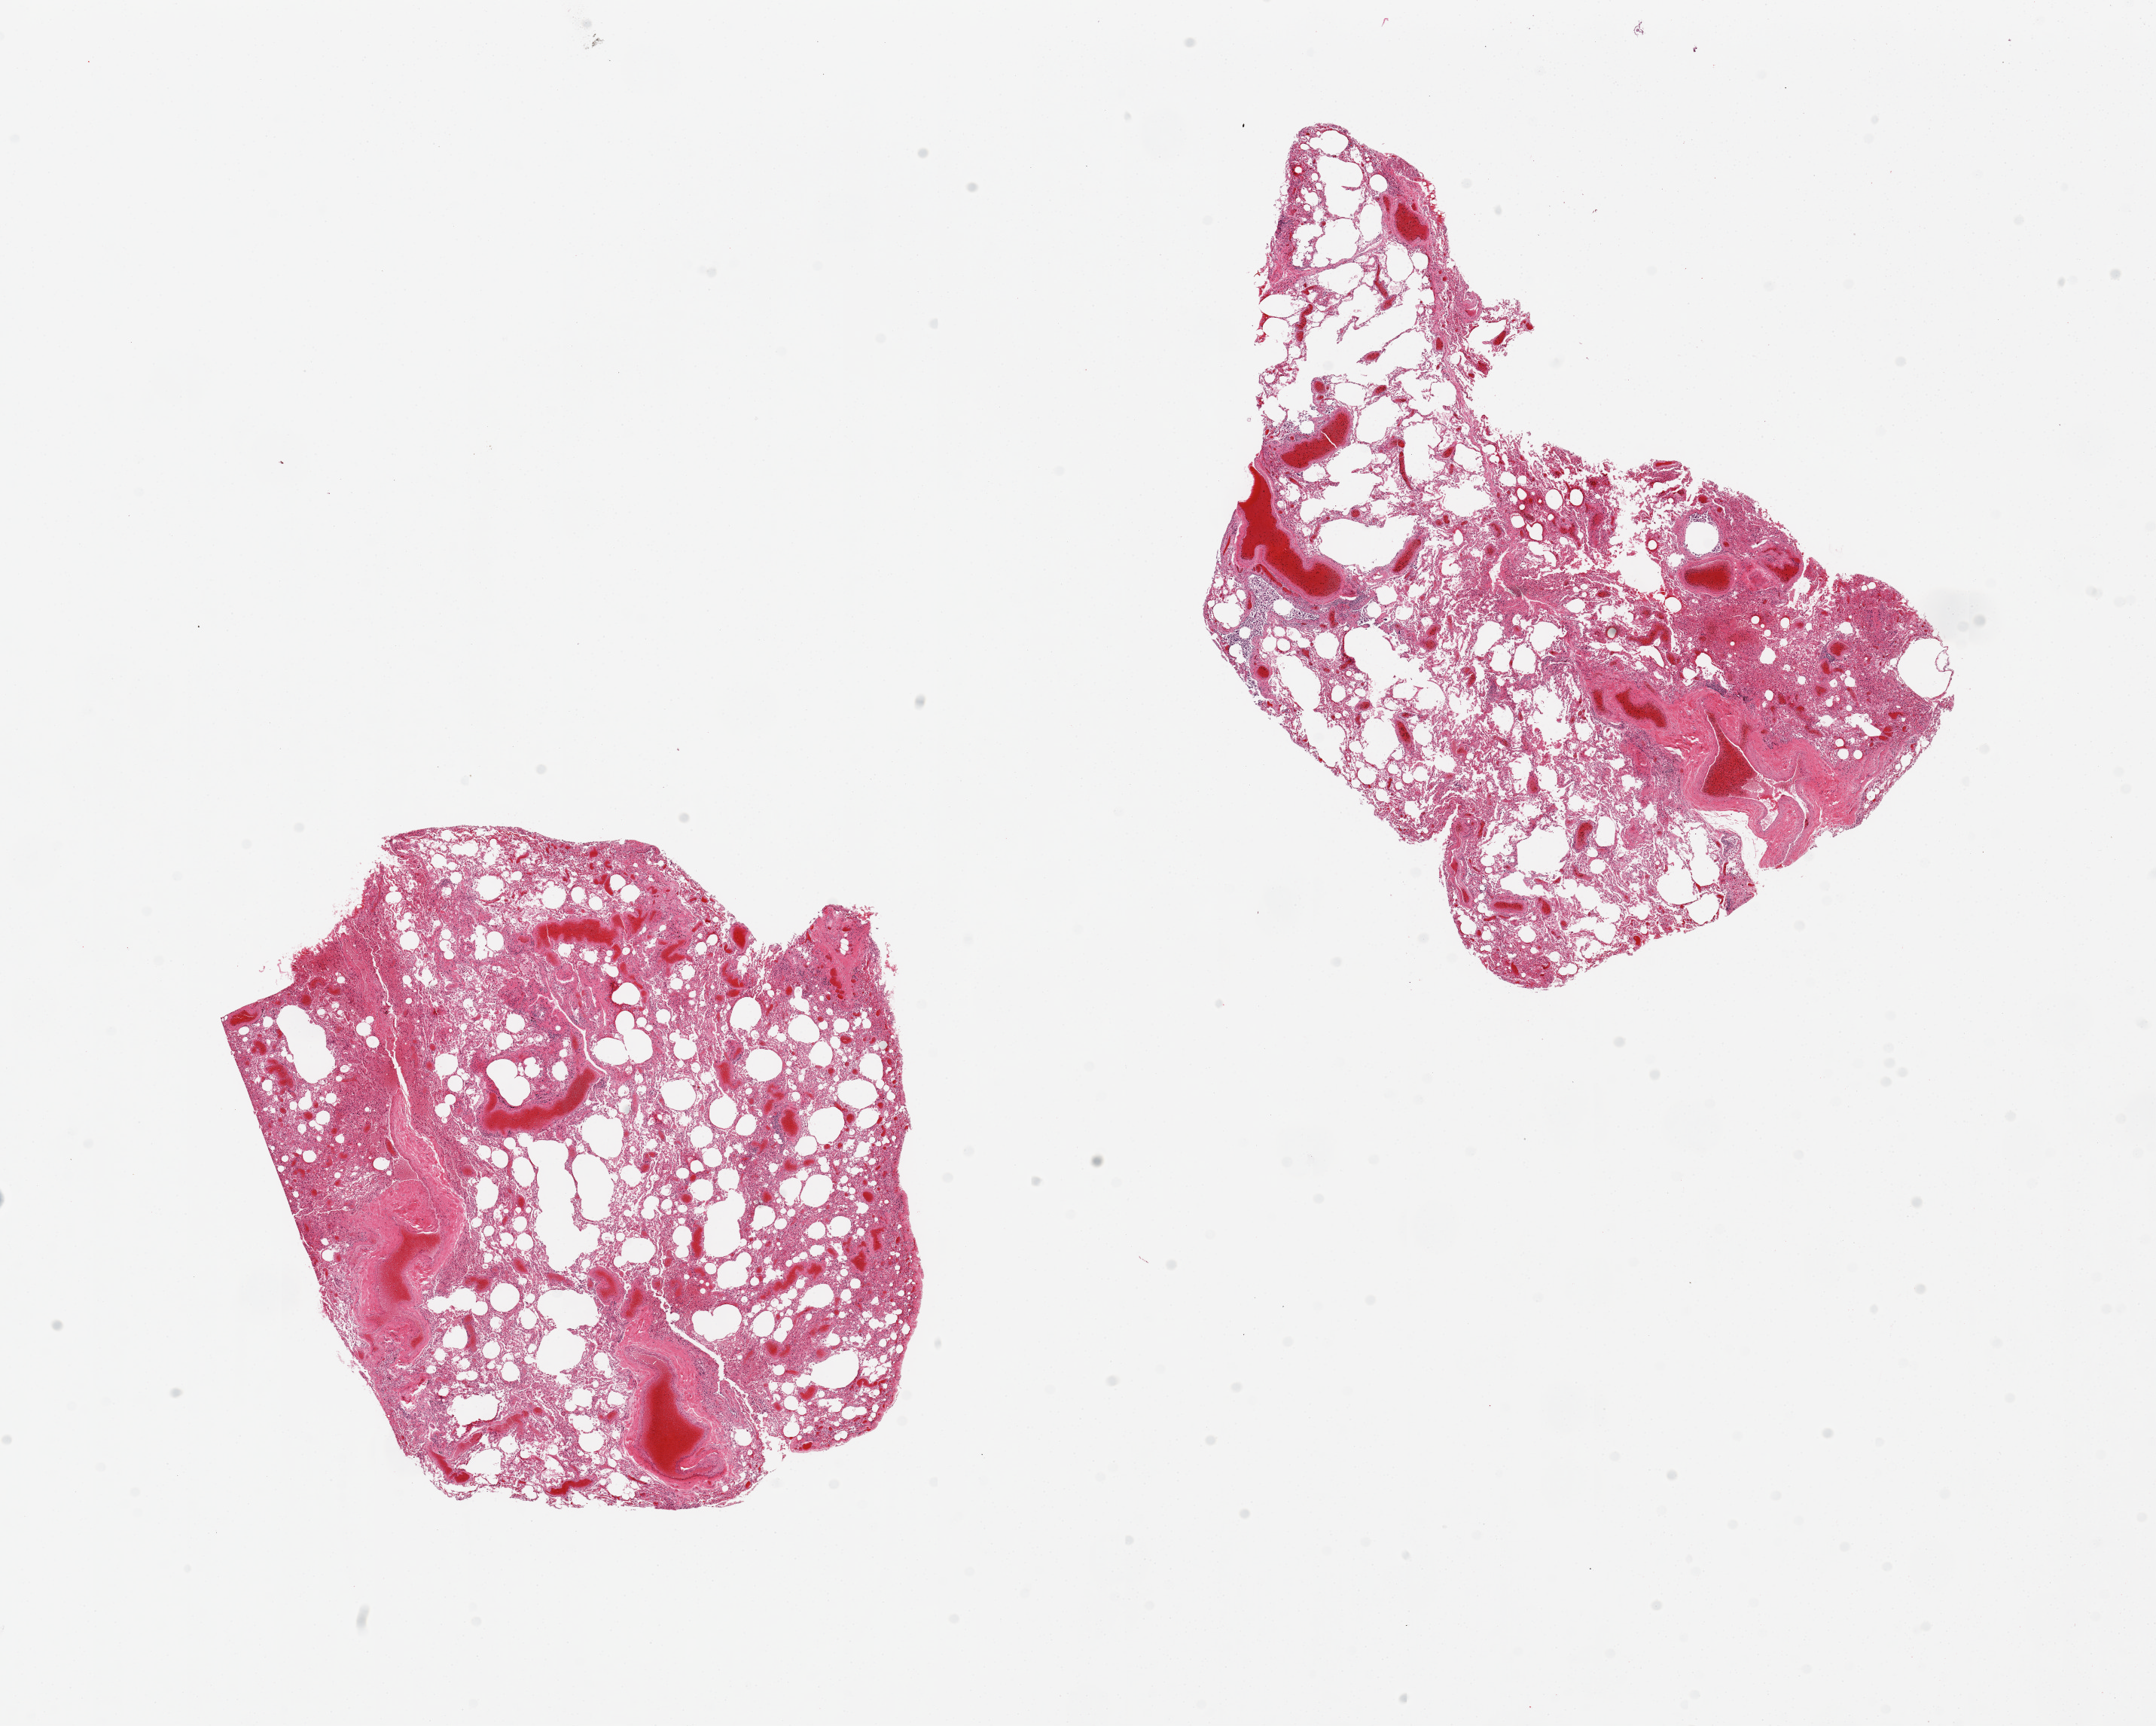
Haematoxylin and eosin whole-slide image, low-resolution overview of the scanned area, about 22.6 x 18.1 mm, PAXgene-fixed paraffin-embedded (PFPE) section, sampled site (target tissue): lung, tissue donor sample. Donor: male.
Review note (as recorded): 2 pieces. moderate congestion.